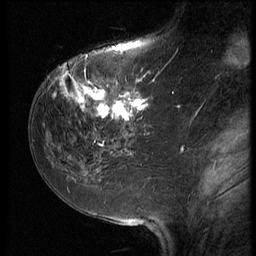
Breast MRI (dynamic contrast-enhanced), one sagittal slice. Position 22 of 64 along the scan axis. 3 images stored at this slice position (order not interpretable as contrast timing). 1.5 T. TE 4.2 ms, TR 9 ms. 2.5 mm slice thickness. 256 × 256 image matrix, field of view 180 × 180 mm. Female patient, age 59 years. Case-level facts recorded for this patient, not image findings: setting: breast cancer imaged before/during neoadjuvant chemotherapy; receptor status: HER2-positive.
Annotated regions visible in this slice (semi-automatic segmentation, software-assisted and operator-edited):
- analysis volume of interest (the breast-tissue region the enhancement analysis was run in; not a lesion): box from (x=54, y=65) to (x=155, y=132) px
- tumour enhancement mask (voxels above the 140 % enhancement threshold inside the analysis volume of interest): (x=58, y=65)–(x=155, y=126)